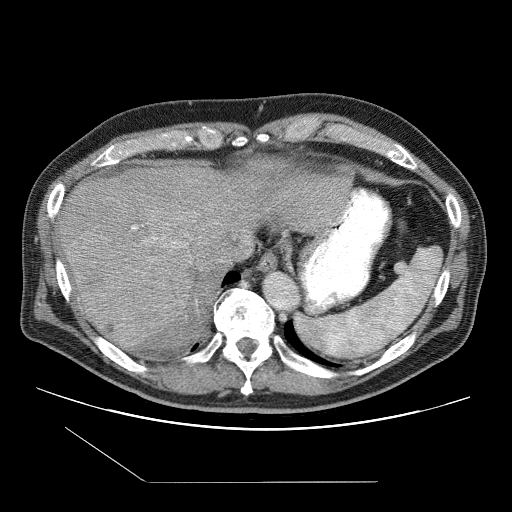
Contrast-enhanced abdominal CT (liver protocol), one axial slice. One of 2 acquisitions stored at this slice position. Soft-tissue window (W 400 / L 40 HU). 2.5 mm slice thickness. 512 × 512 image matrix. From the clinical record (not read from this slice): diagnosis: hepatocellular carcinoma (patient treated with transarterial chemoembolisation; whether this scan precedes or follows treatment is not stated here); TNM stage (as recorded): Stage-IIIB.
Annotated regions visible in this slice (semi-automatic segmentation, software-assisted and operator-edited):
- liver parenchyma outside the tumour (the mass and vessels are separate outlines, so this box may not span the whole liver): bounding box <56,156,350,350> (left, top, right, bottom; pixels)
- mass: <67,229,193,347>
- liver vessels: <131,212,346,239>